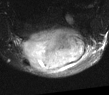
MRI of an extremity soft-tissue mass, one axial slice; slice 19 of 52 in the series (ordered by position); T2-weighted fat-saturated; MR volume resampled by the dataset authors to the PET/CT grid (not the native acquisition matrix); 3.27 mm slice thickness; 109 × 95 image matrix, field of view 106 × 93 mm. Male patient. Case-level facts recorded for this patient, not image findings: histological type: synovial sarcoma; site of the primary tumour: left poplietal fossa.
Annotated regions visible in this slice (expert contour drawn on MRI and transferred to this co-registered scan by the dataset authors):
- gross tumour volume (mass): box from (x=19, y=28) to (x=89, y=73) px